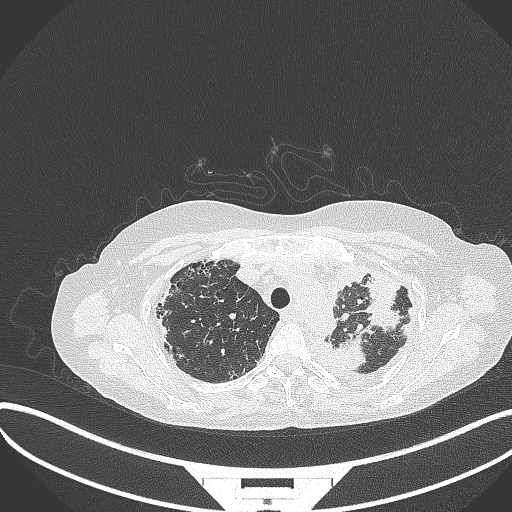
Chest CT, one axial slice; position 270 of 373 along the scan axis; reconstruction kernel B70f; 120 kVp; lung window (W 1500 / L -600 HU); 1 mm slice thickness; 512 × 512 image matrix, field of view 400 × 400 mm. Female patient, age 56 years. From the clinical record (not read from this slice): clinical TNM (as recorded): T1 N0 M0.
Structures marked on this image (rectangle marked by the reading radiologist):
- lung tumour (recorded histology: adenocarcinoma): bounding box (x1, y1, x2, y2) in pixels: (336, 336, 371, 377)
- lung tumour (recorded histology: adenocarcinoma): (357, 265, 404, 331)